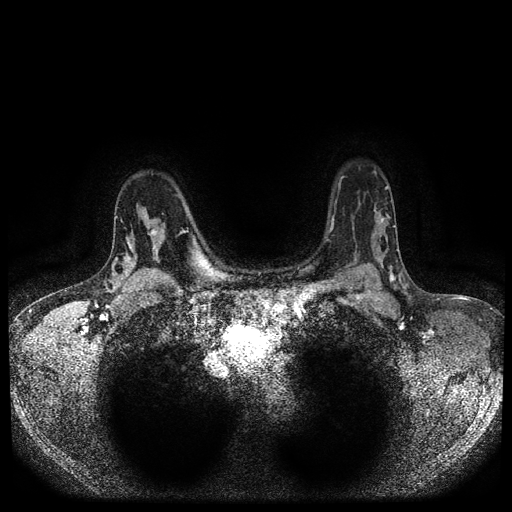
Breast MRI (dynamic contrast-enhanced, multi-phase), one axial slice; position 75 of 116 along the scan axis; dynamic contrast-enhanced series, time point 2 of 5 at this slice position (early post-contrast); 1.5 T; TE 2.6 ms, TR 5.4 ms; 2 mm slice thickness; 512 × 512 image matrix, field of view 340 × 340 mm. Patient: female, 47 years.
Annotated regions visible in this slice (semi-automatic segmentation, software-assisted and operator-edited):
- breast lesion (labelled 'tumour' in the annotation; benign lesions carry a separate 'benign' label): bounding box <146,228,160,238> (left, top, right, bottom; pixels)